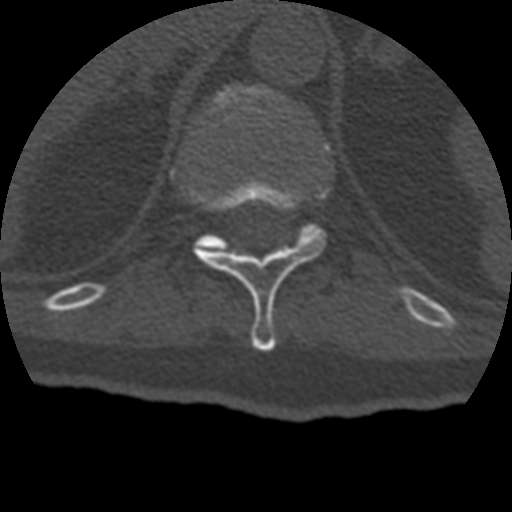
CT including the spine, one axial slice; position 188 of 399 along the scan axis; reconstruction kernel STANDARD; bone window (W 1800 / L 400 HU); 512 × 512 image matrix. Patient age 69 years. From the clinical record (not read from this slice): primary cancer: prostate.
Annotated regions visible in this slice (semi-automatic segmentation, software-assisted and operator-edited):
- T11 vertebra: bounding box (x1, y1, x2, y2) in pixels: (190, 178, 327, 351)
- T12 vertebra: (199, 86, 314, 248)